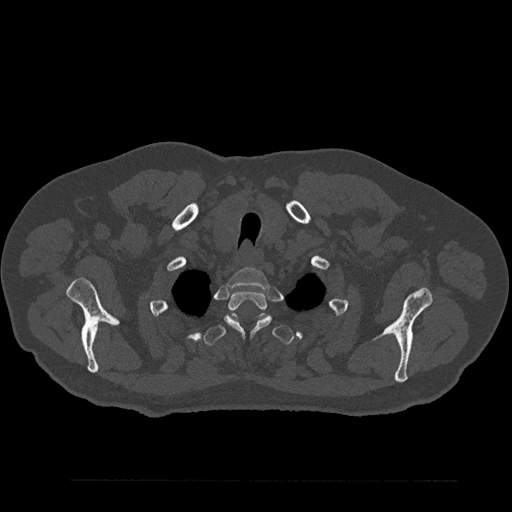
CT including the spine, one axial slice; slice 713 of 797 in the series (ordered by position); bone window (W 1800 / L 400 HU); 0.5 mm slice thickness; 512 × 512 image matrix, field of view 430 × 430 mm. Male patient, age 61 years. Case-level facts recorded for this patient, not image findings: primary cancer: prostate.
Annotated regions visible in this slice (semi-automatic segmentation, software-assisted and operator-edited):
- T1 vertebra: bounding box [x1, y1, x2, y2] px = [227, 268, 270, 288]
- T2 vertebra: [224, 291, 272, 336]
- T3 vertebra: [204, 313, 294, 345]